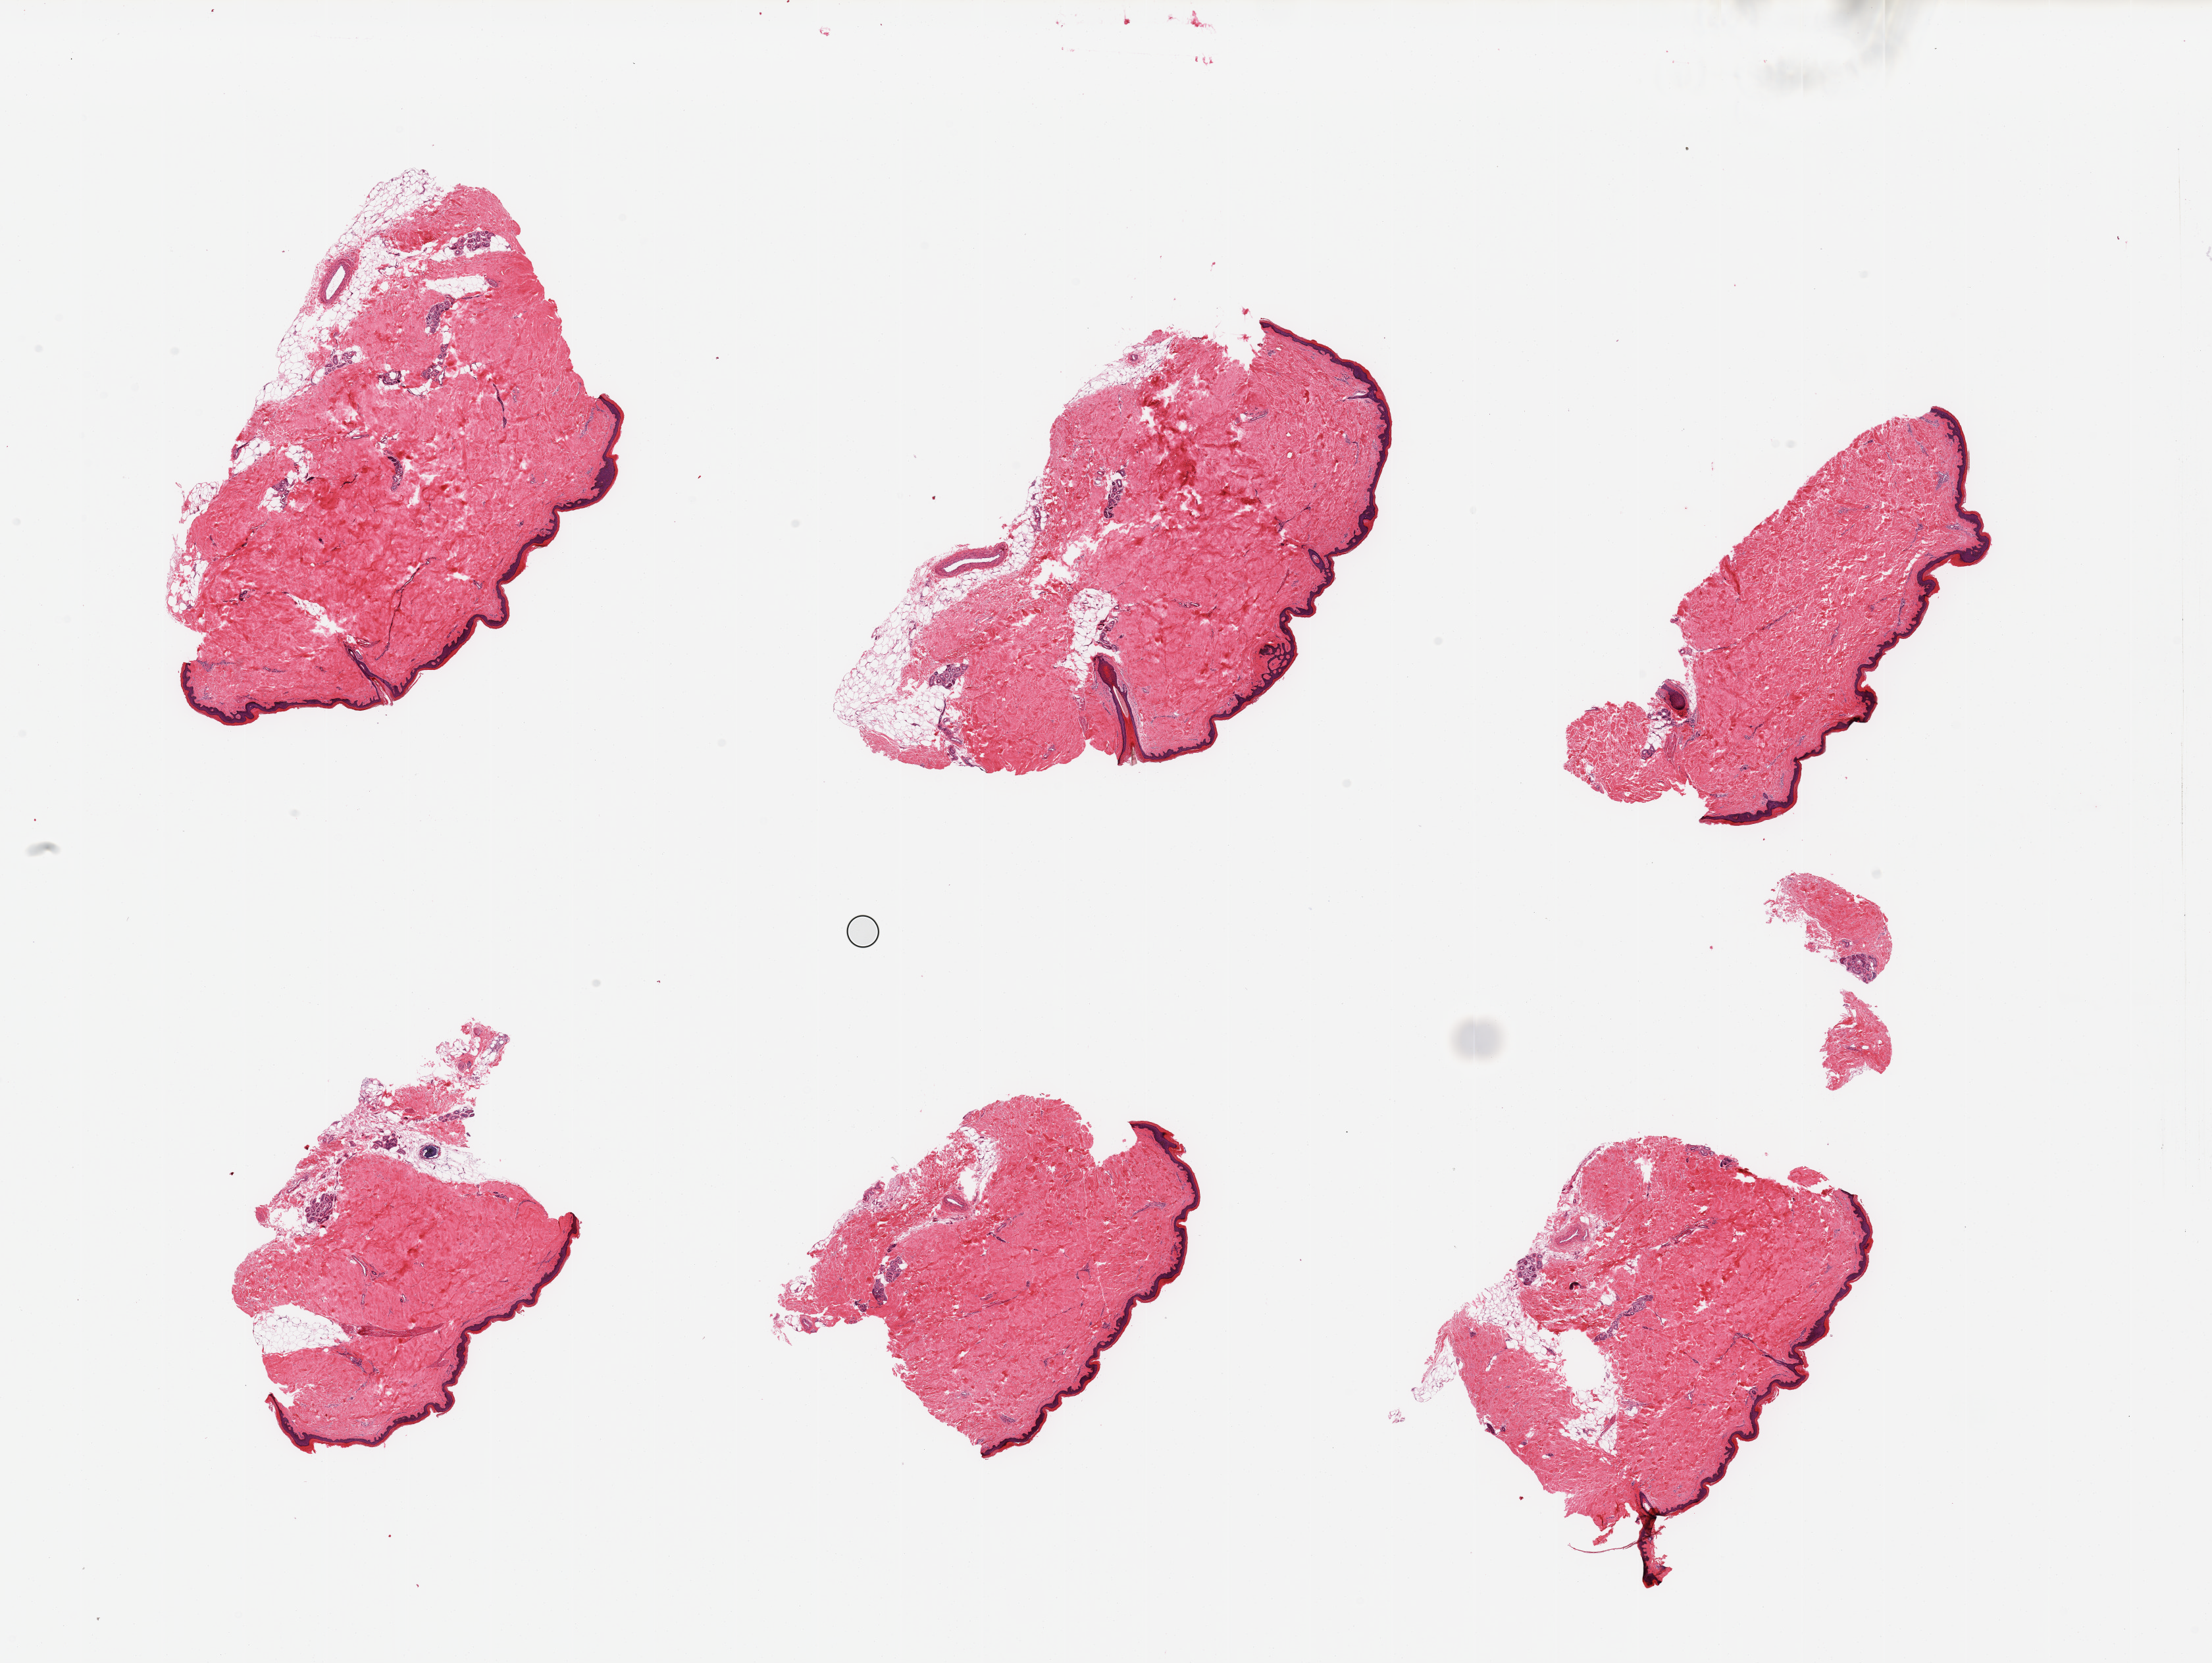
H&E whole-slide image, brightfield, a low-resolution overview of the entire scanned area, about 26.6 x 20.0 mm (from a 20x scan); PAXgene-fixed, paraffin-embedded tissue; target tissue: skin of lower leg; tissue donor sample. Male donor.
- pathologist's review note for this sample: 6 pieces; includes variable internal/external fat up to ~15%, epidermis measures 38 microns